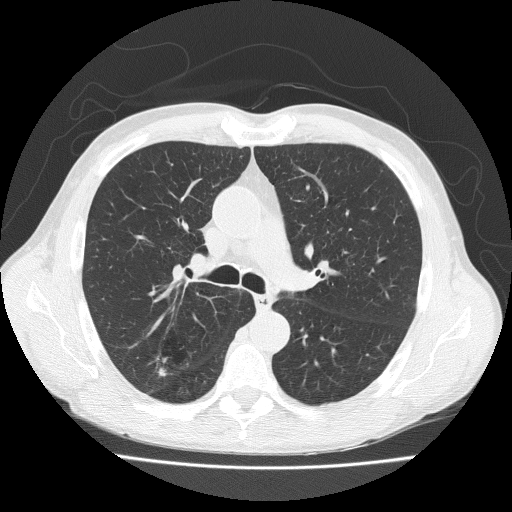
Low-dose screening chest CT, axial slice; first (baseline) screen; lung window (W 1500 / L -600 HU); 2 mm slice thickness; lung (sharp) reconstruction kernel (FC51); 120 kVp; slice 75 of 203 in the series; 512 × 512 image matrix. Male participant, aged 73 years at enrolment. Current smoker at enrolment.
Expert reader's lesion annotation, bounding box [x1, y1, x2, y2] px = [144, 331, 193, 378]. No non-calcified nodule or mass ≥4 mm was recorded by the screening reader at this exam. Later outcome: lung cancer diagnosed 777 days after this screen — adenosquamous carcinoma, right upper lobe, well differentiated (G1), stage IA (AJCC 6th edition), 20 mm at pathology.